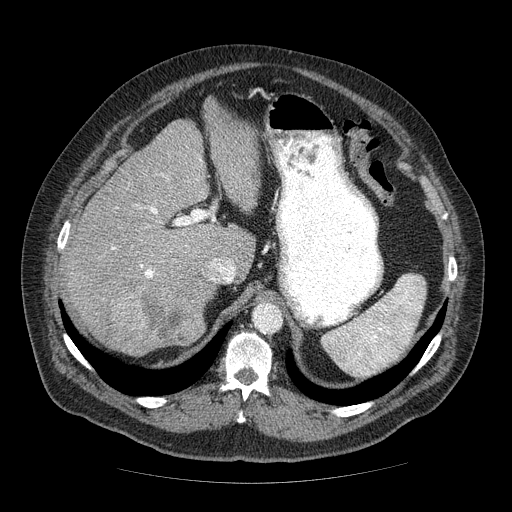
Contrast-enhanced abdominal CT (liver protocol), one axial slice; 120 kVp; soft-tissue window (W 400 / L 40 HU); 512 × 512 image matrix, field of view 420 × 420 mm. Case-level facts recorded for this patient, not image findings: diagnosis: hepatocellular carcinoma (patient treated with transarterial chemoembolisation; whether this scan precedes or follows treatment is not stated here); TNM stage (as recorded): Stage-IIIA; Child-Pugh class: A; tumour nodularity: multinodular; tumour size: 7 cm.
Annotated regions visible in this slice (semi-automatically segmented with operator editing):
- liver parenchyma outside the tumour (the mass and vessels are separate outlines, so this box may not span the whole liver): bounding box <64,104,260,344> (left, top, right, bottom; pixels)
- mass: <105,273,216,357>
- liver vessels: <111,159,202,278>